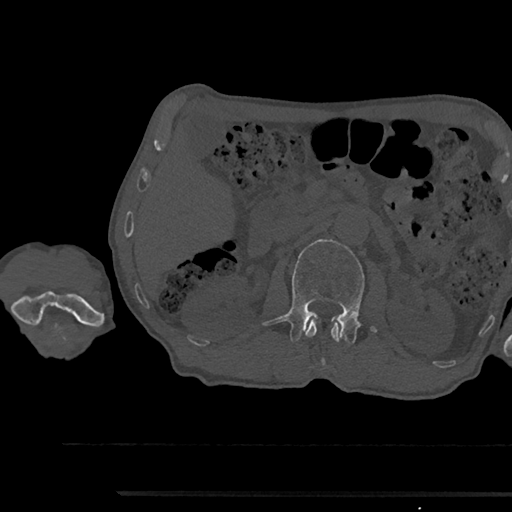
CT including the spine, one axial slice. Slice 589 of 797 in the series (ordered by position). 120 kVp. Bone window (W 1800 / L 400 HU). 0.5 mm slice thickness. 512 × 512 image matrix. Male patient, age 79 years. From the clinical record (not read from this slice): primary cancer: prostate.
Outlined on this slice (semi-automatic segmentation, software-assisted and operator-edited):
- L1 vertebra: bounding box [x1, y1, x2, y2] px = [305, 319, 341, 342]
- L2 vertebra: [263, 239, 376, 344]